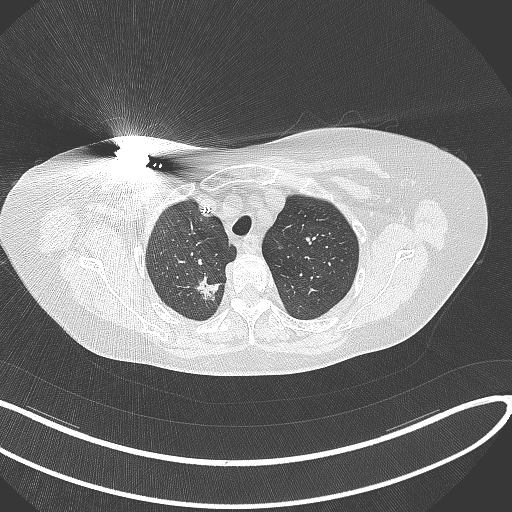
Chest CT, one axial slice; position 274 of 316 along the scan axis; reconstruction kernel B70f; 120 kVp; lung window (W 1500 / L -600 HU); 1 mm slice thickness; 512 × 512 image matrix. Female patient, age 72 years. Case-level facts recorded for this patient, not image findings: clinical TNM (as recorded): T1c N0 M0.
Annotated regions visible in this slice (rectangle marked by the reading radiologist):
- lung tumour (recorded histology: adenocarcinoma): bounding box (x1, y1, x2, y2) in pixels: (193, 275, 221, 305)